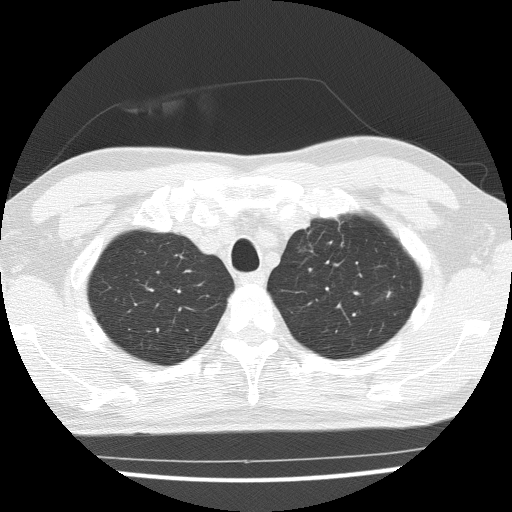
Low-dose screening chest CT, one axial slice. Slice 125 of 154 in the series (ordered by position). Reconstruction kernel FC51. Lung window (W 1500 / L -600 HU). 2 mm slice thickness. 512 × 512 image matrix, field of view 330 × 330 mm.
Structures marked on this image (manually delineated by an expert):
- lesion 1 (tumor, upper lobe of left lung): box from (x=387, y=292) to (x=391, y=297) px